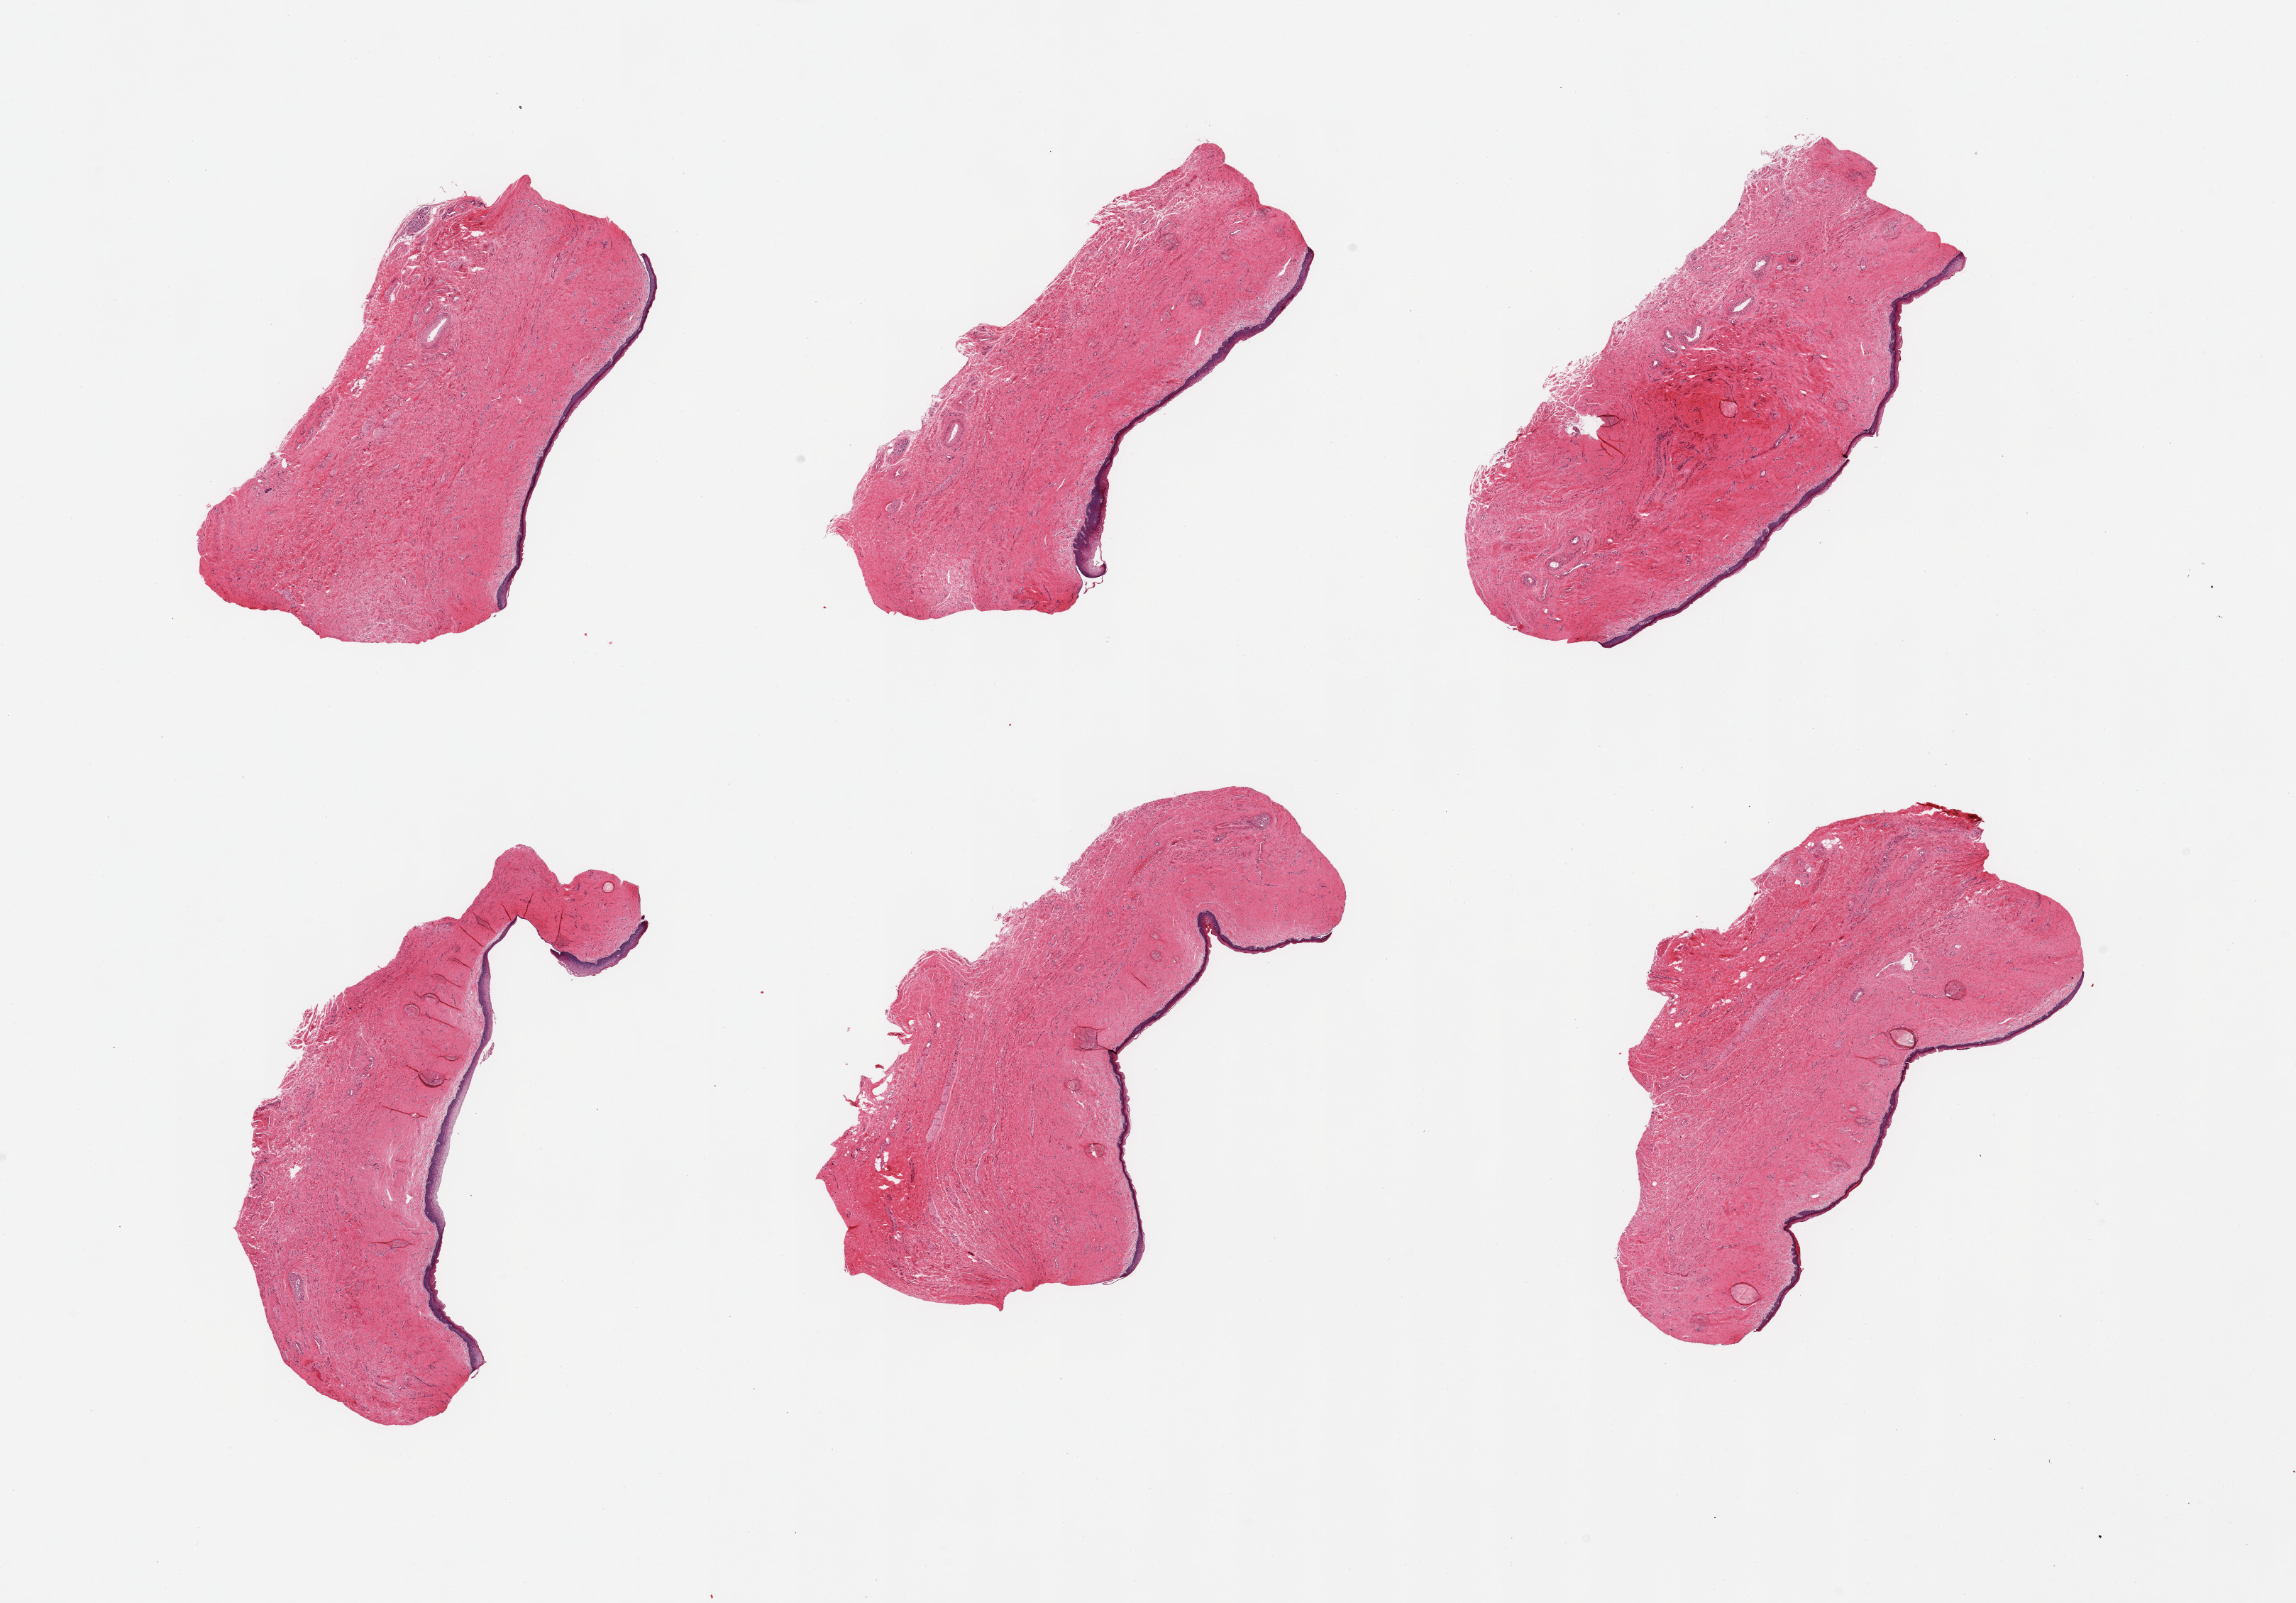
Whole-slide image, haematoxylin and eosin stain, low-resolution overview of the scanned area, about 25.6 x 17.9 mm (acquisition: 20x scan). PAXgene-fixed paraffin-embedded (PFPE) section. Target tissue: vagina. Donor tissue sample. Female donor.
• pathologist's review note for this sample: 6 pieces